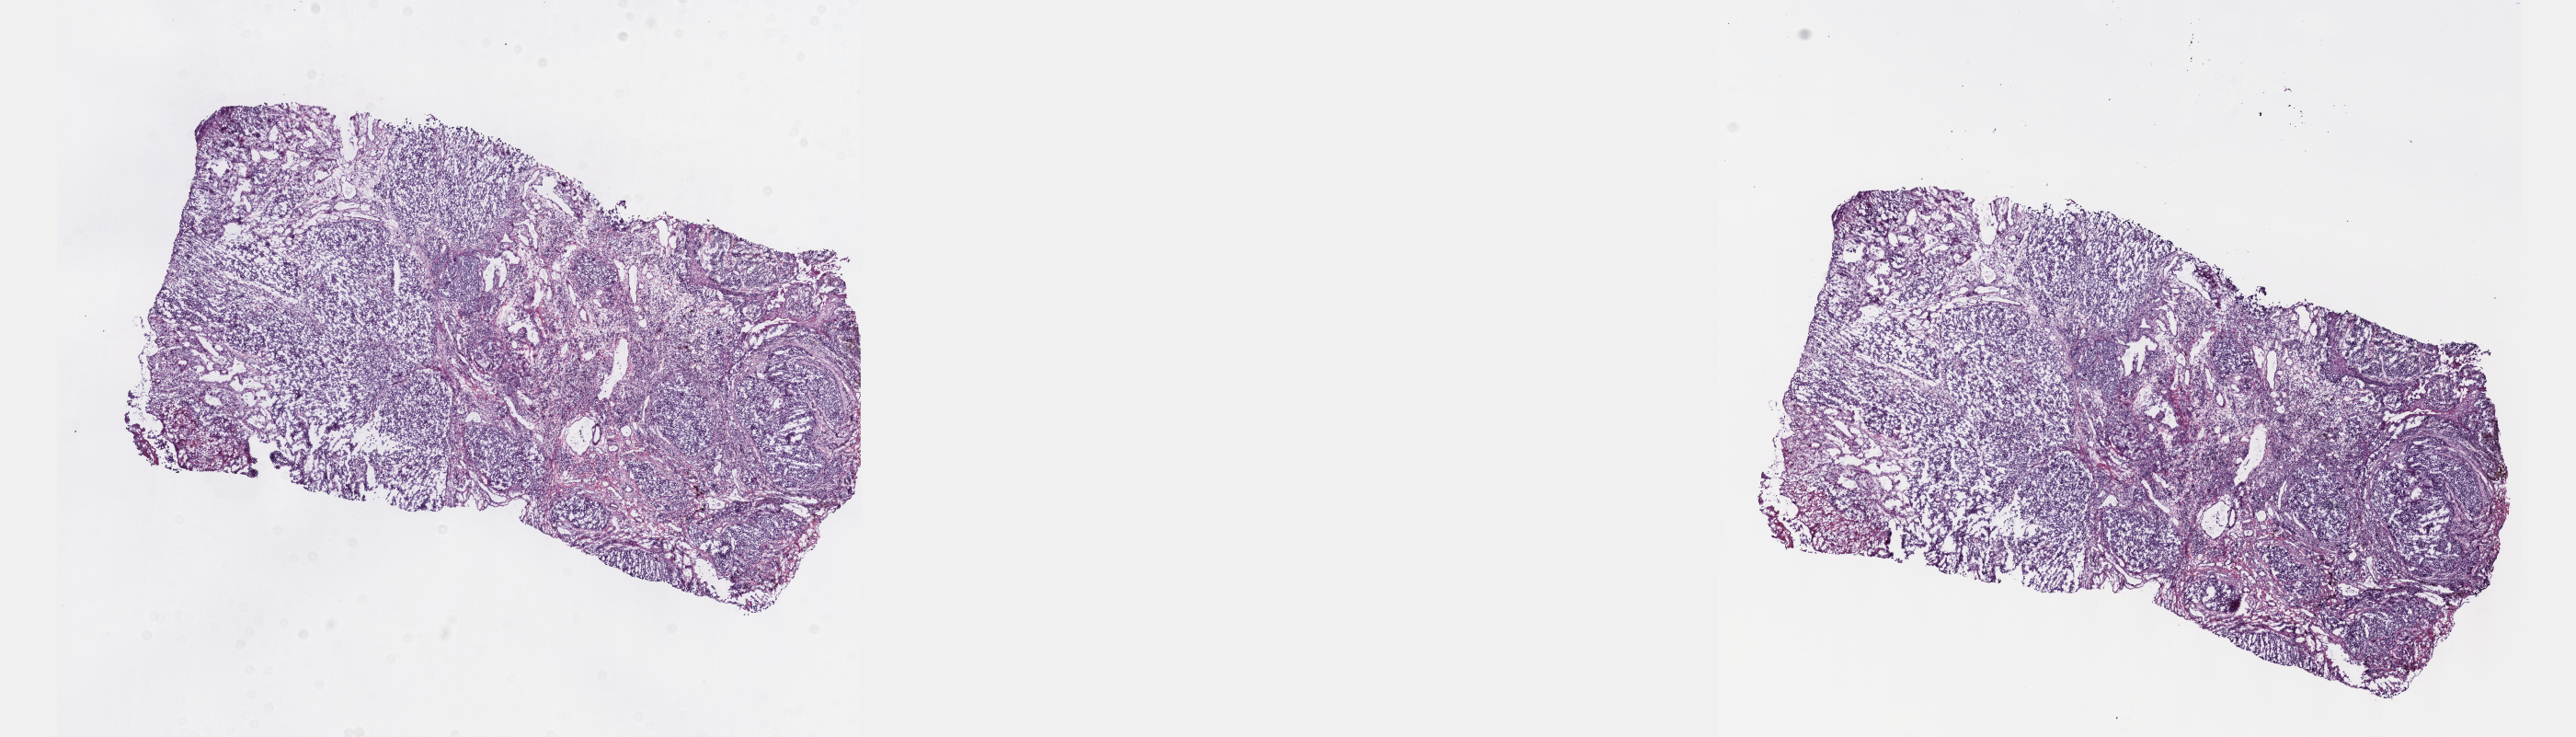
Digitized H&E-stained tissue section (whole slide), a low-resolution overview of the entire scanned area, about 22.6 x 6.5 mm; frozen section from the top of the tissue portion; skin, primary tumour sample. Patient: male, age at initial diagnosis 51 years. Pathologist review of this section (percent, as recorded): tumour cells 100%, tumour nuclei 90%, normal cells 0%, stromal cells 0%, necrosis 0%. Infiltration values recorded for this section: lymphocyte infiltration 0%, monocyte infiltration 0%, neutrophil infiltration 0%.
• histologic diagnosis: Malignant melanoma, NOS